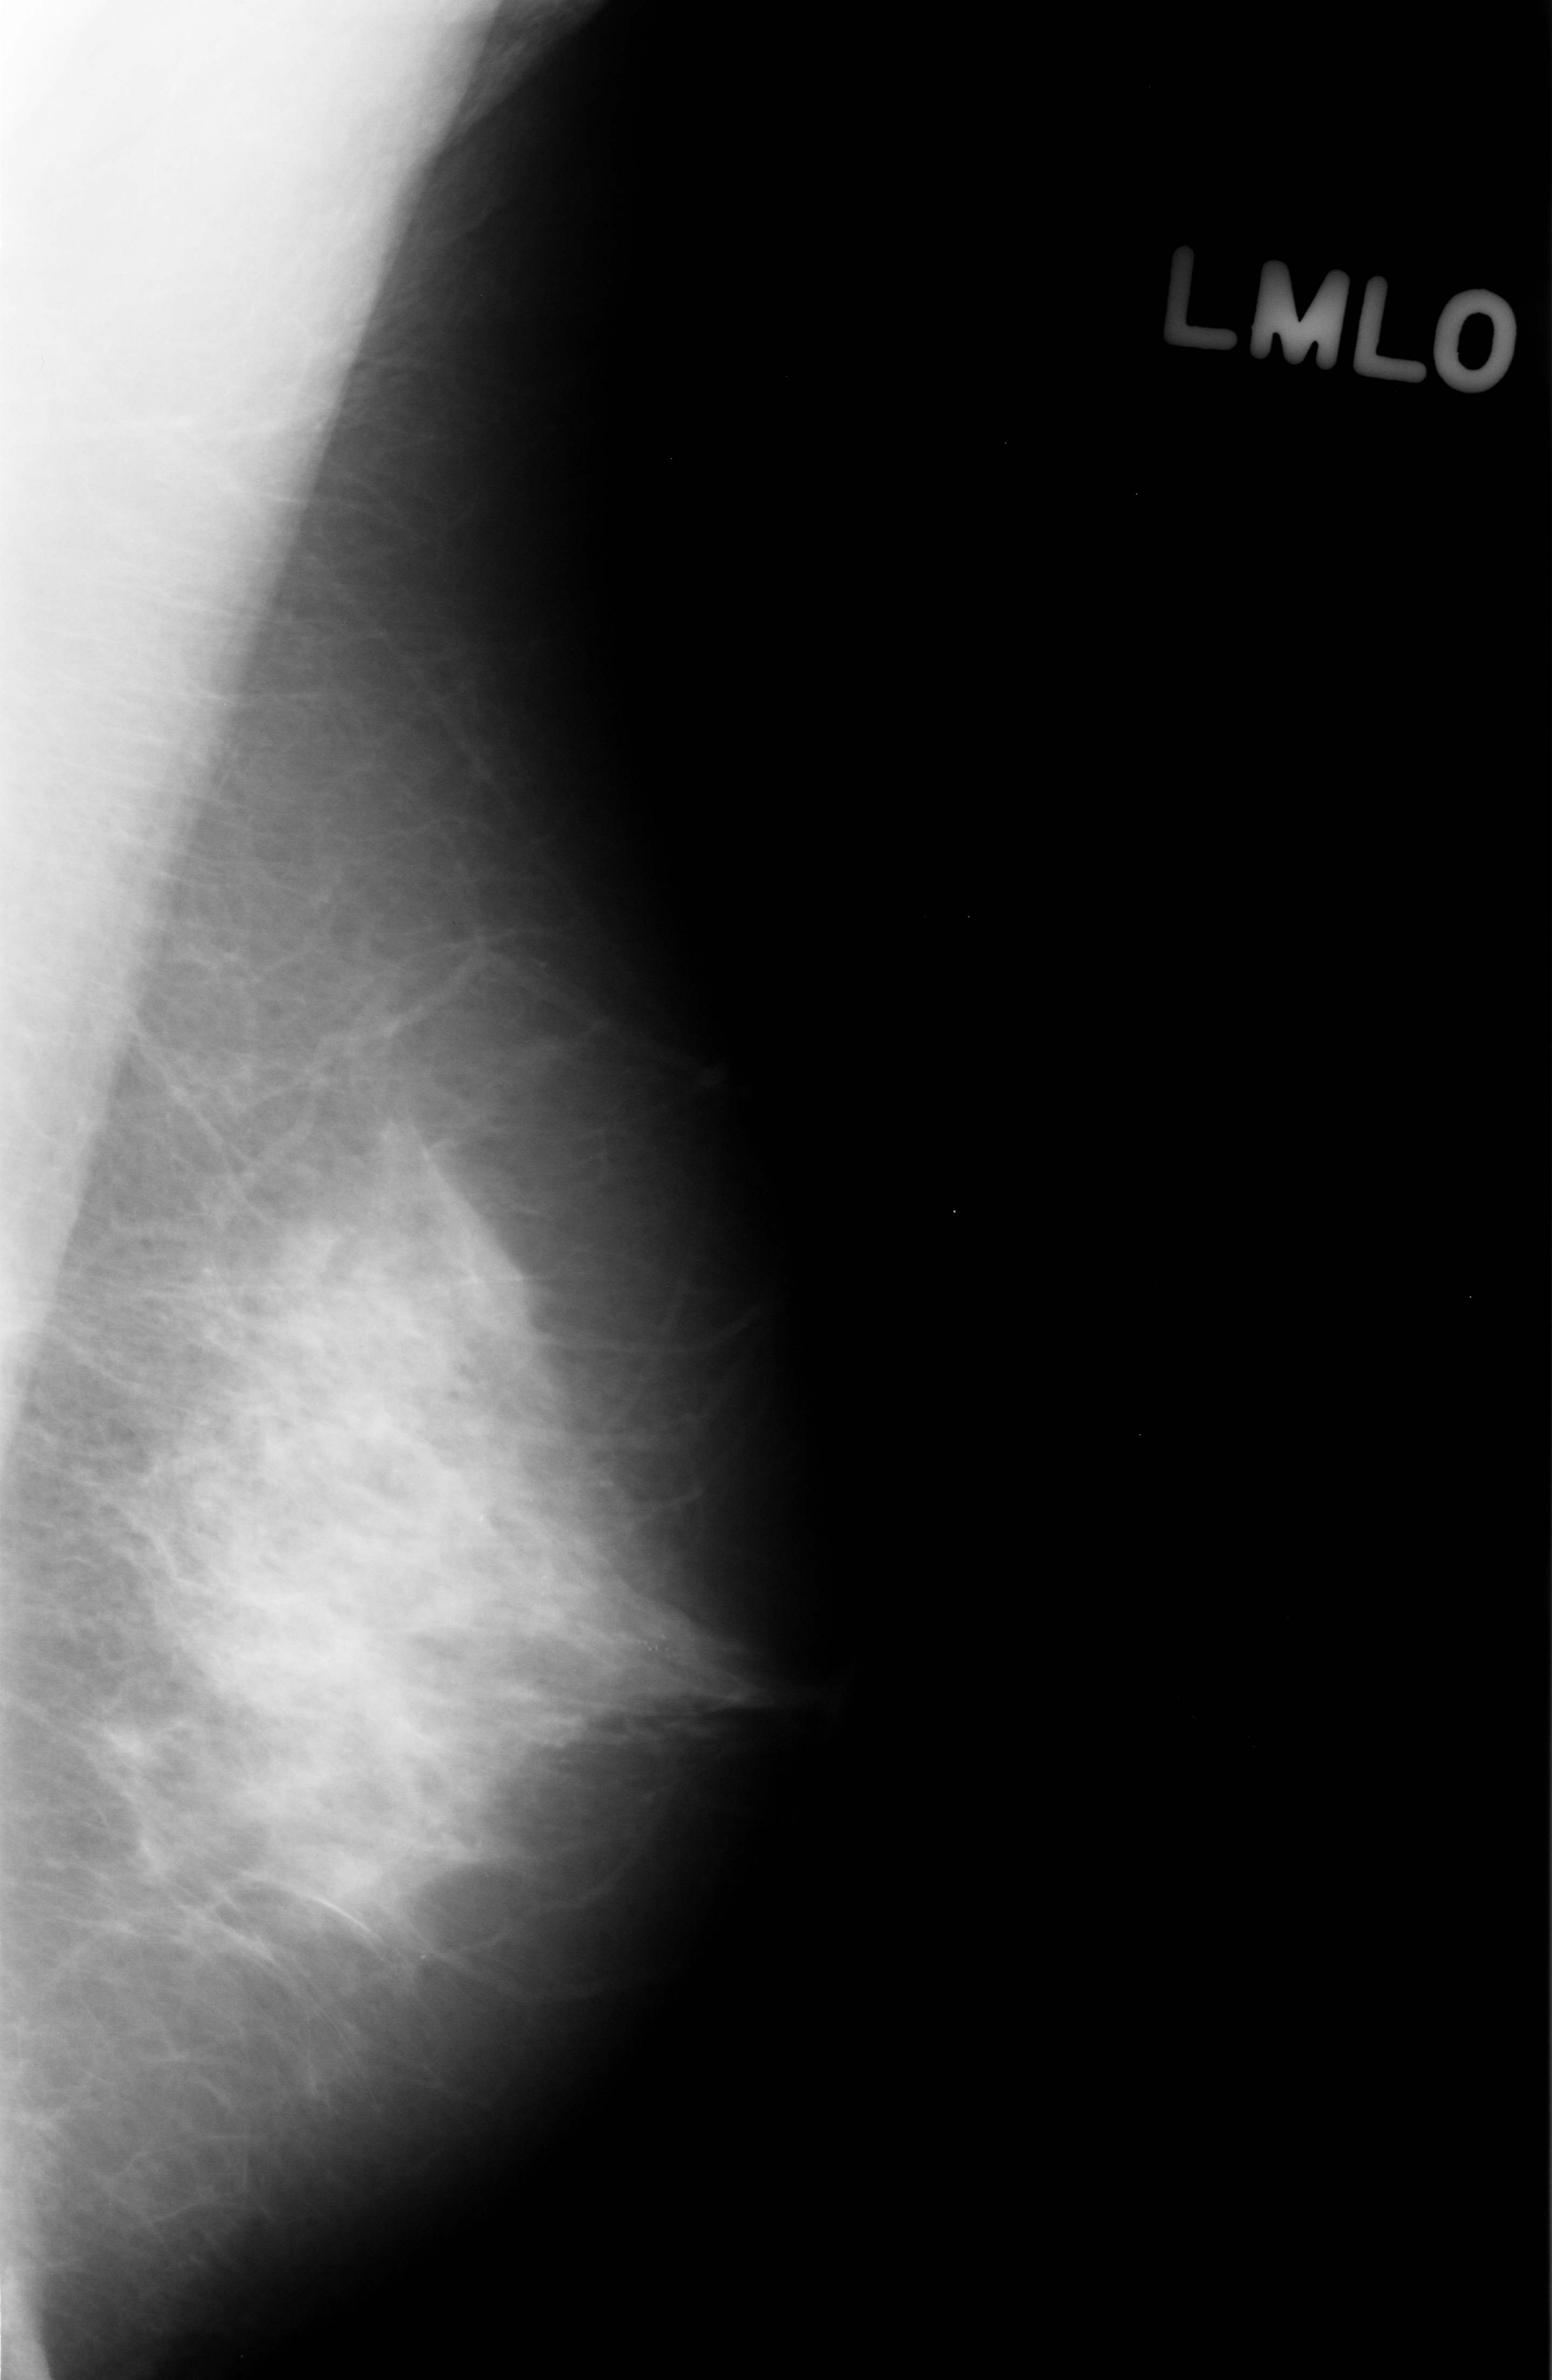
Digitized screen-film mammogram, left breast, MLO view, BI-RADS breast density category 3 (scale 1–4).
Abnormality record for this image: calcifications, morphology punctate, distribution clustered; BI-RADS assessment category 4; pathology result (as recorded, not read from the image): benign.